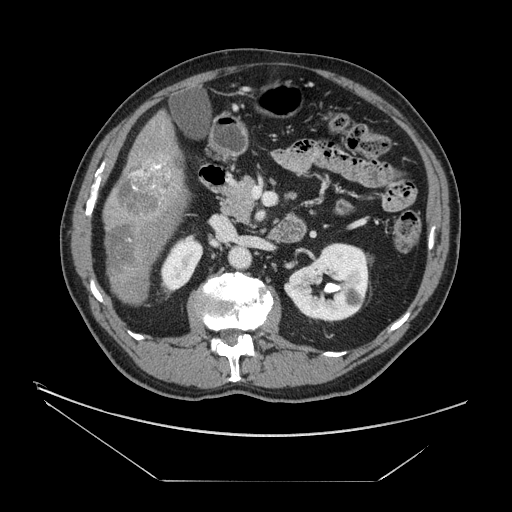
Contrast-enhanced abdominal CT, one axial slice; slice 65 of 161 in the series (ordered by position); reconstruction kernel STANDARD; intravenous contrast given; soft-tissue window (W 400 / L 40 HU); 512 × 512 image matrix, field of view 440 × 440 mm. Male patient, age 65 years. From the clinical record (not read from this slice): diagnosis: colorectal cancer liver metastases, imaged before liver resection; multiple liver metastases: yes; largest metastasis: 4.2 cm; disease in both lobes: yes.
Outlined on this slice (expert manual segmentation):
- liver: bounding box (x1, y1, x2, y2) in pixels: (104, 114, 190, 305)
- portal vein (with intrahepatic branches): (133, 163, 169, 193)
- liver metastasis: (109, 227, 137, 271)
- liver metastasis: (118, 160, 173, 219)